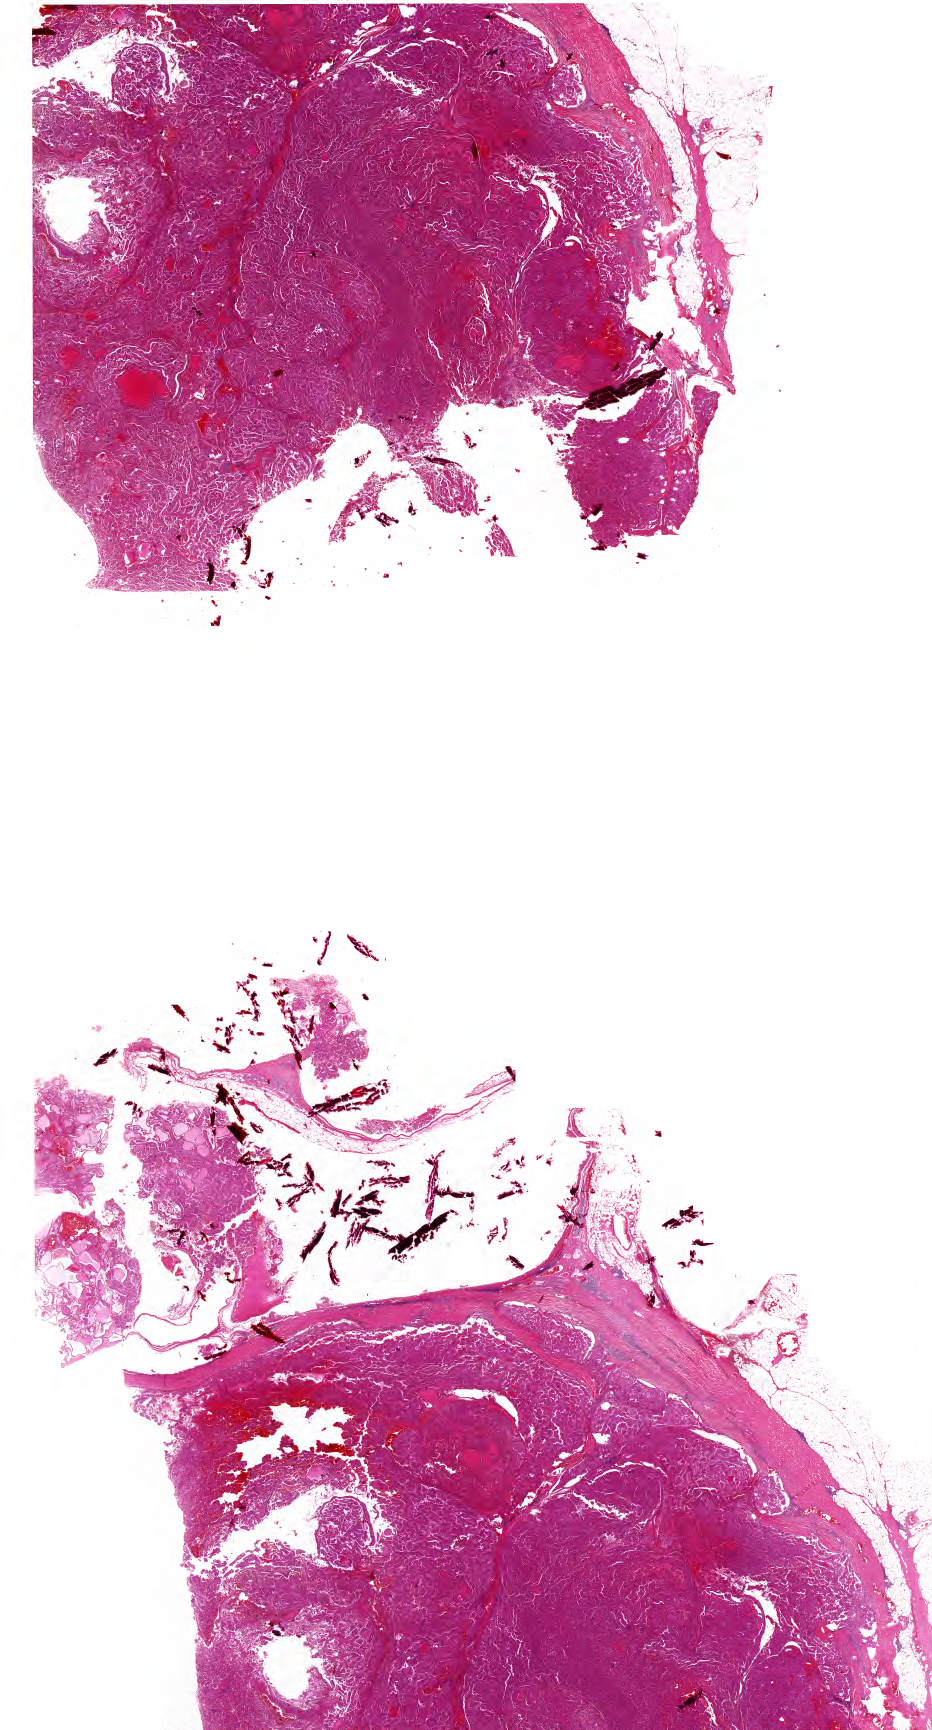
Digitized H&E-stained tissue section (whole slide), whole scanned area (about 23.2 x 43.1 mm) shown as a low-resolution overview; formalin-fixed paraffin-embedded (FFPE) diagnostic section; kidney, primary tumour sample. Patient: male, age at initial diagnosis 59 years.
Pathologic diagnosis: Papillary adenocarcinoma, NOS. Laterality: right.